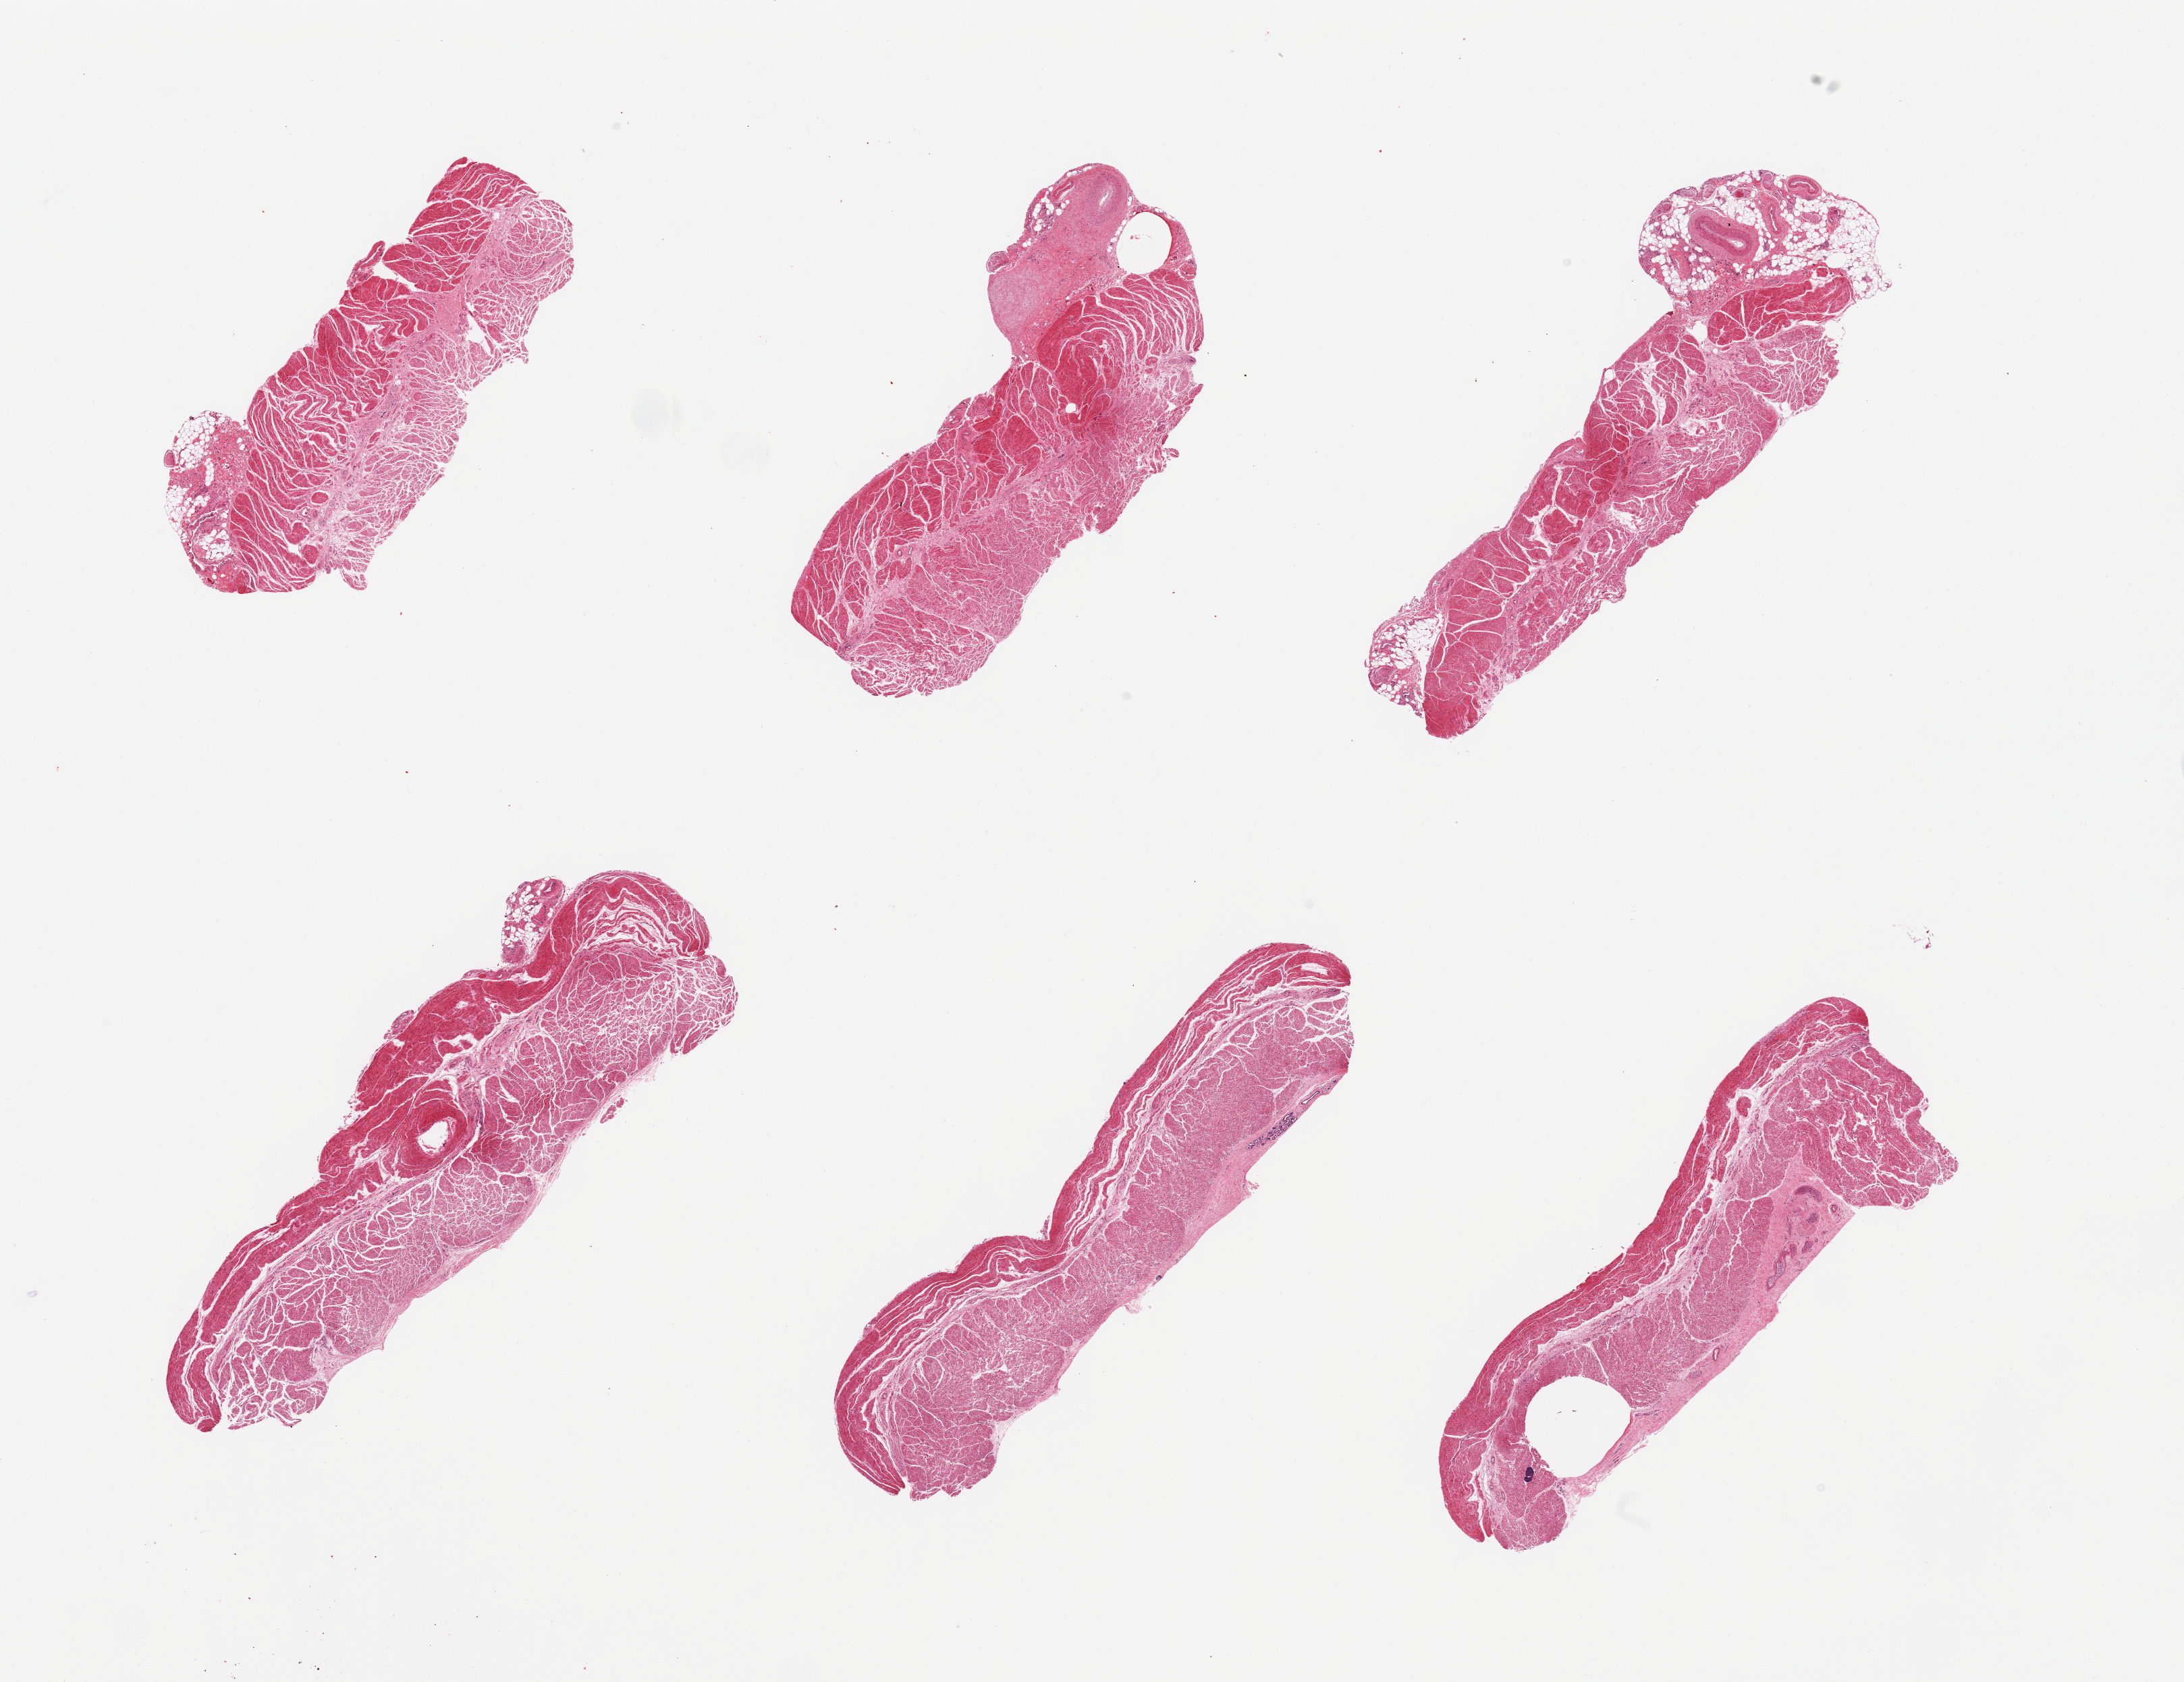
Whole-slide image, H&E stain — low-resolution overview of the scanned area, about 25.6 x 19.7 mm, PAXgene-fixed paraffin-embedded (PFPE) section, section of esophageal muscle (target tissue), donor tissue sample. Donor: female.
- review note (as recorded): 6 pieces; well trimmed